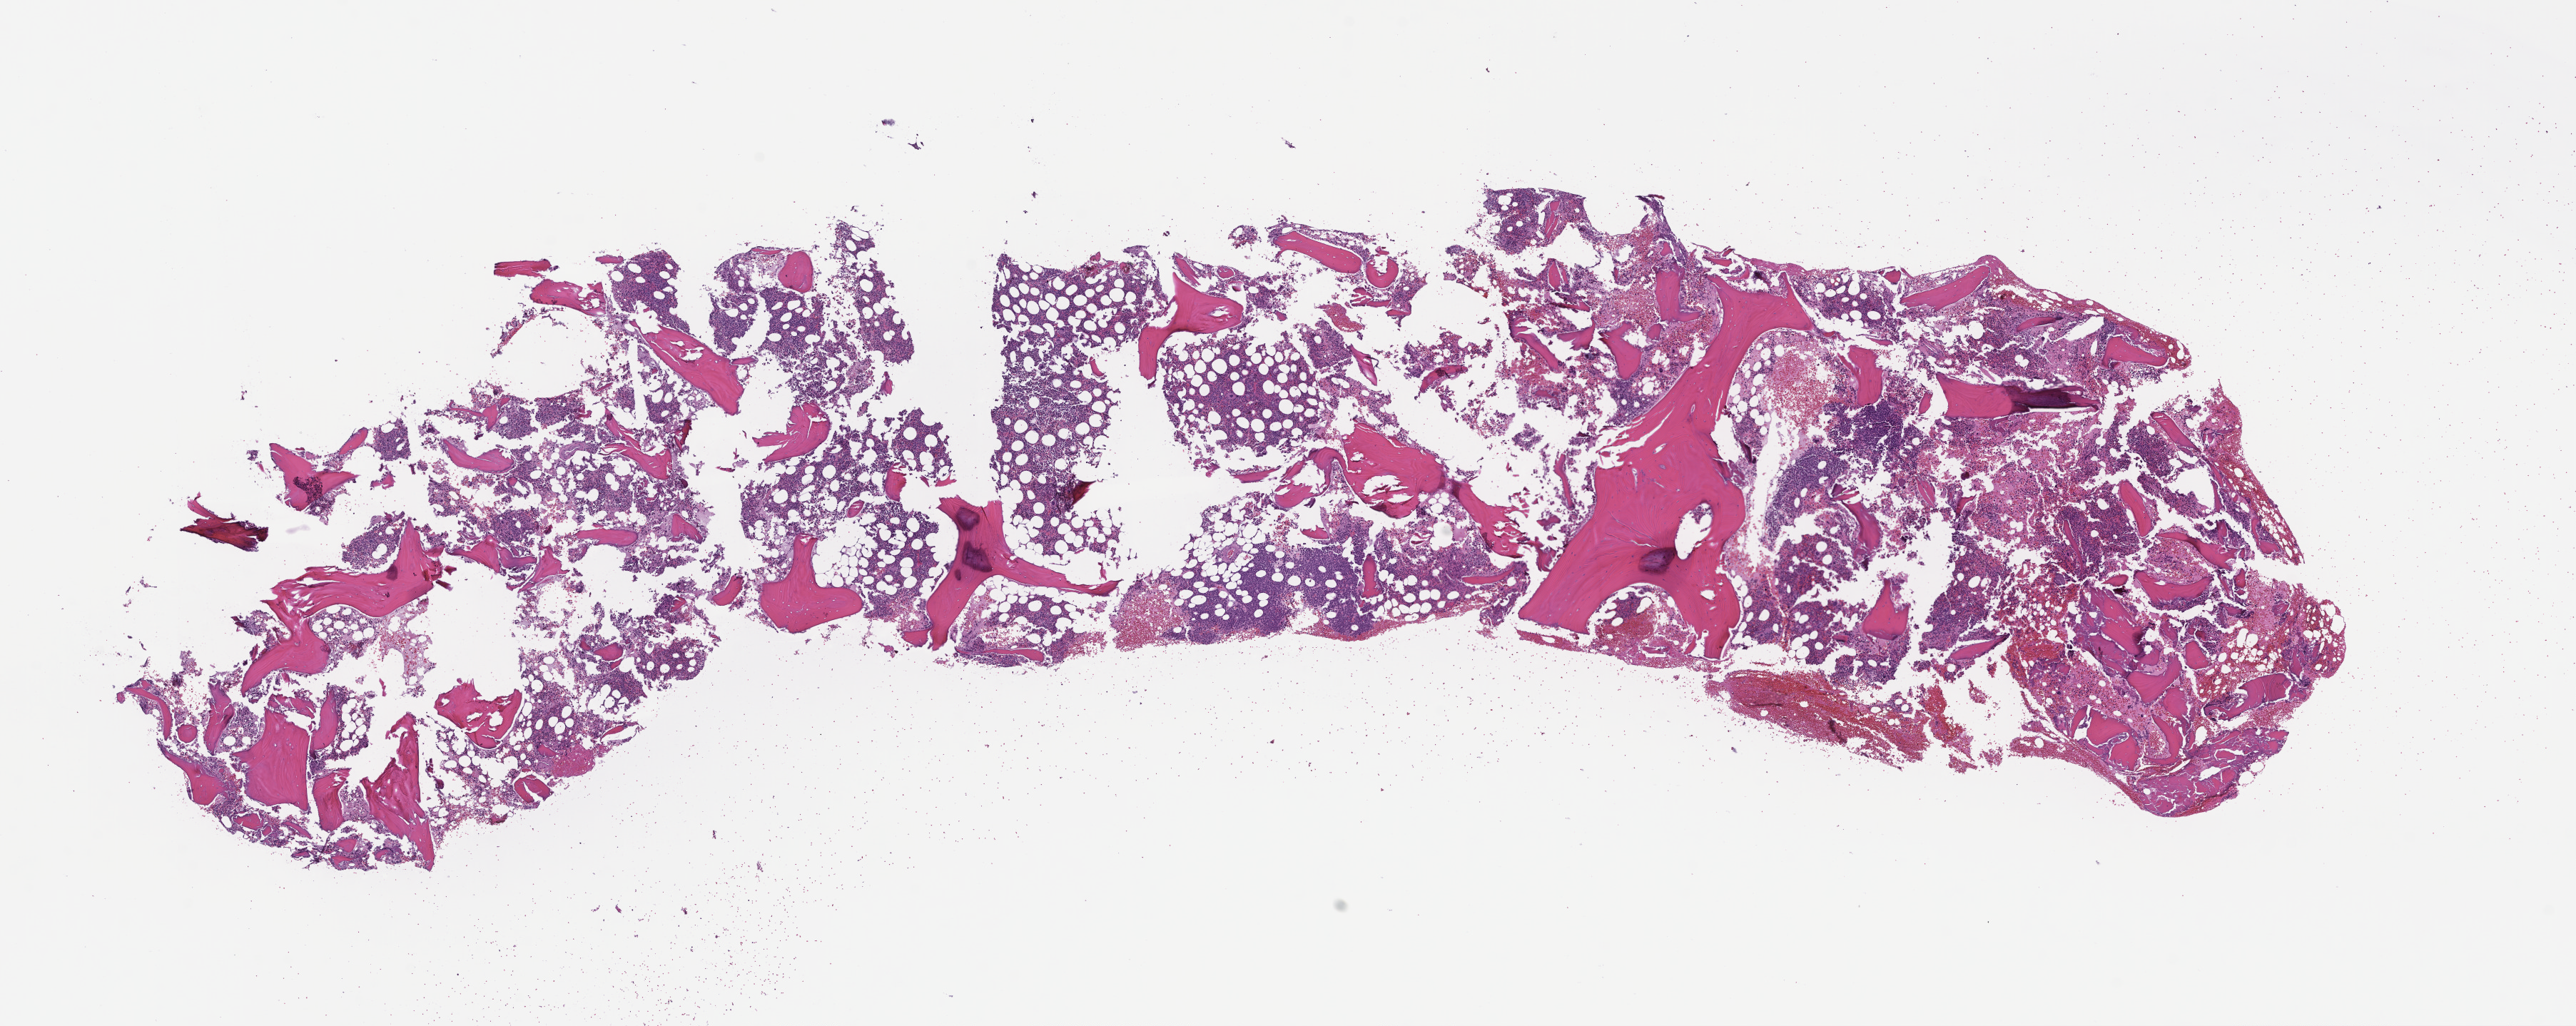
Whole-slide image, H&E stain — a low-resolution overview of the entire scanned area, about 14.6 x 5.8 mm; FFPE section; tissue site: bone; specimen time point: archival tissue. Patient sex: female.
This section: primary tumor. Diagnosis: Plasma Cell Myeloma.